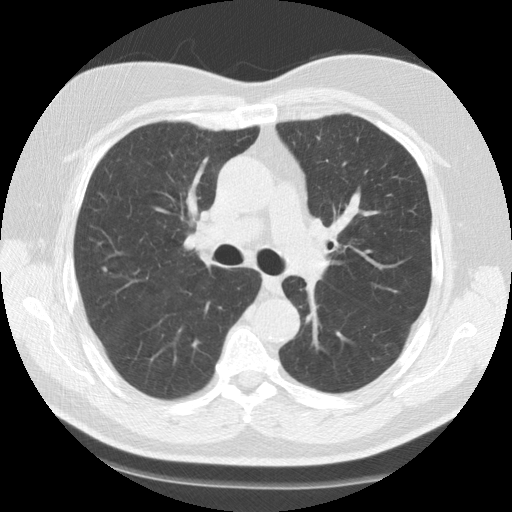
Low-dose screening chest CT, axial slice. Second screening round (one year after baseline). Lung window (W 1500 / L -600 HU). 2.5 mm slice thickness. Male, age 65 years at enrolment.
Expert reader's lesion annotation, bounding box [x1, y1, x2, y2] px = [96, 262, 114, 278]. No non-calcified nodule or mass ≥4 mm was recorded by the screening reader at this exam. Participant outcome: lung cancer diagnosed 432 days after this screen — adenocarcinoma, NOS, right upper lobe, poorly differentiated (G3), stage IA (AJCC 6th edition), 17 mm at pathology.